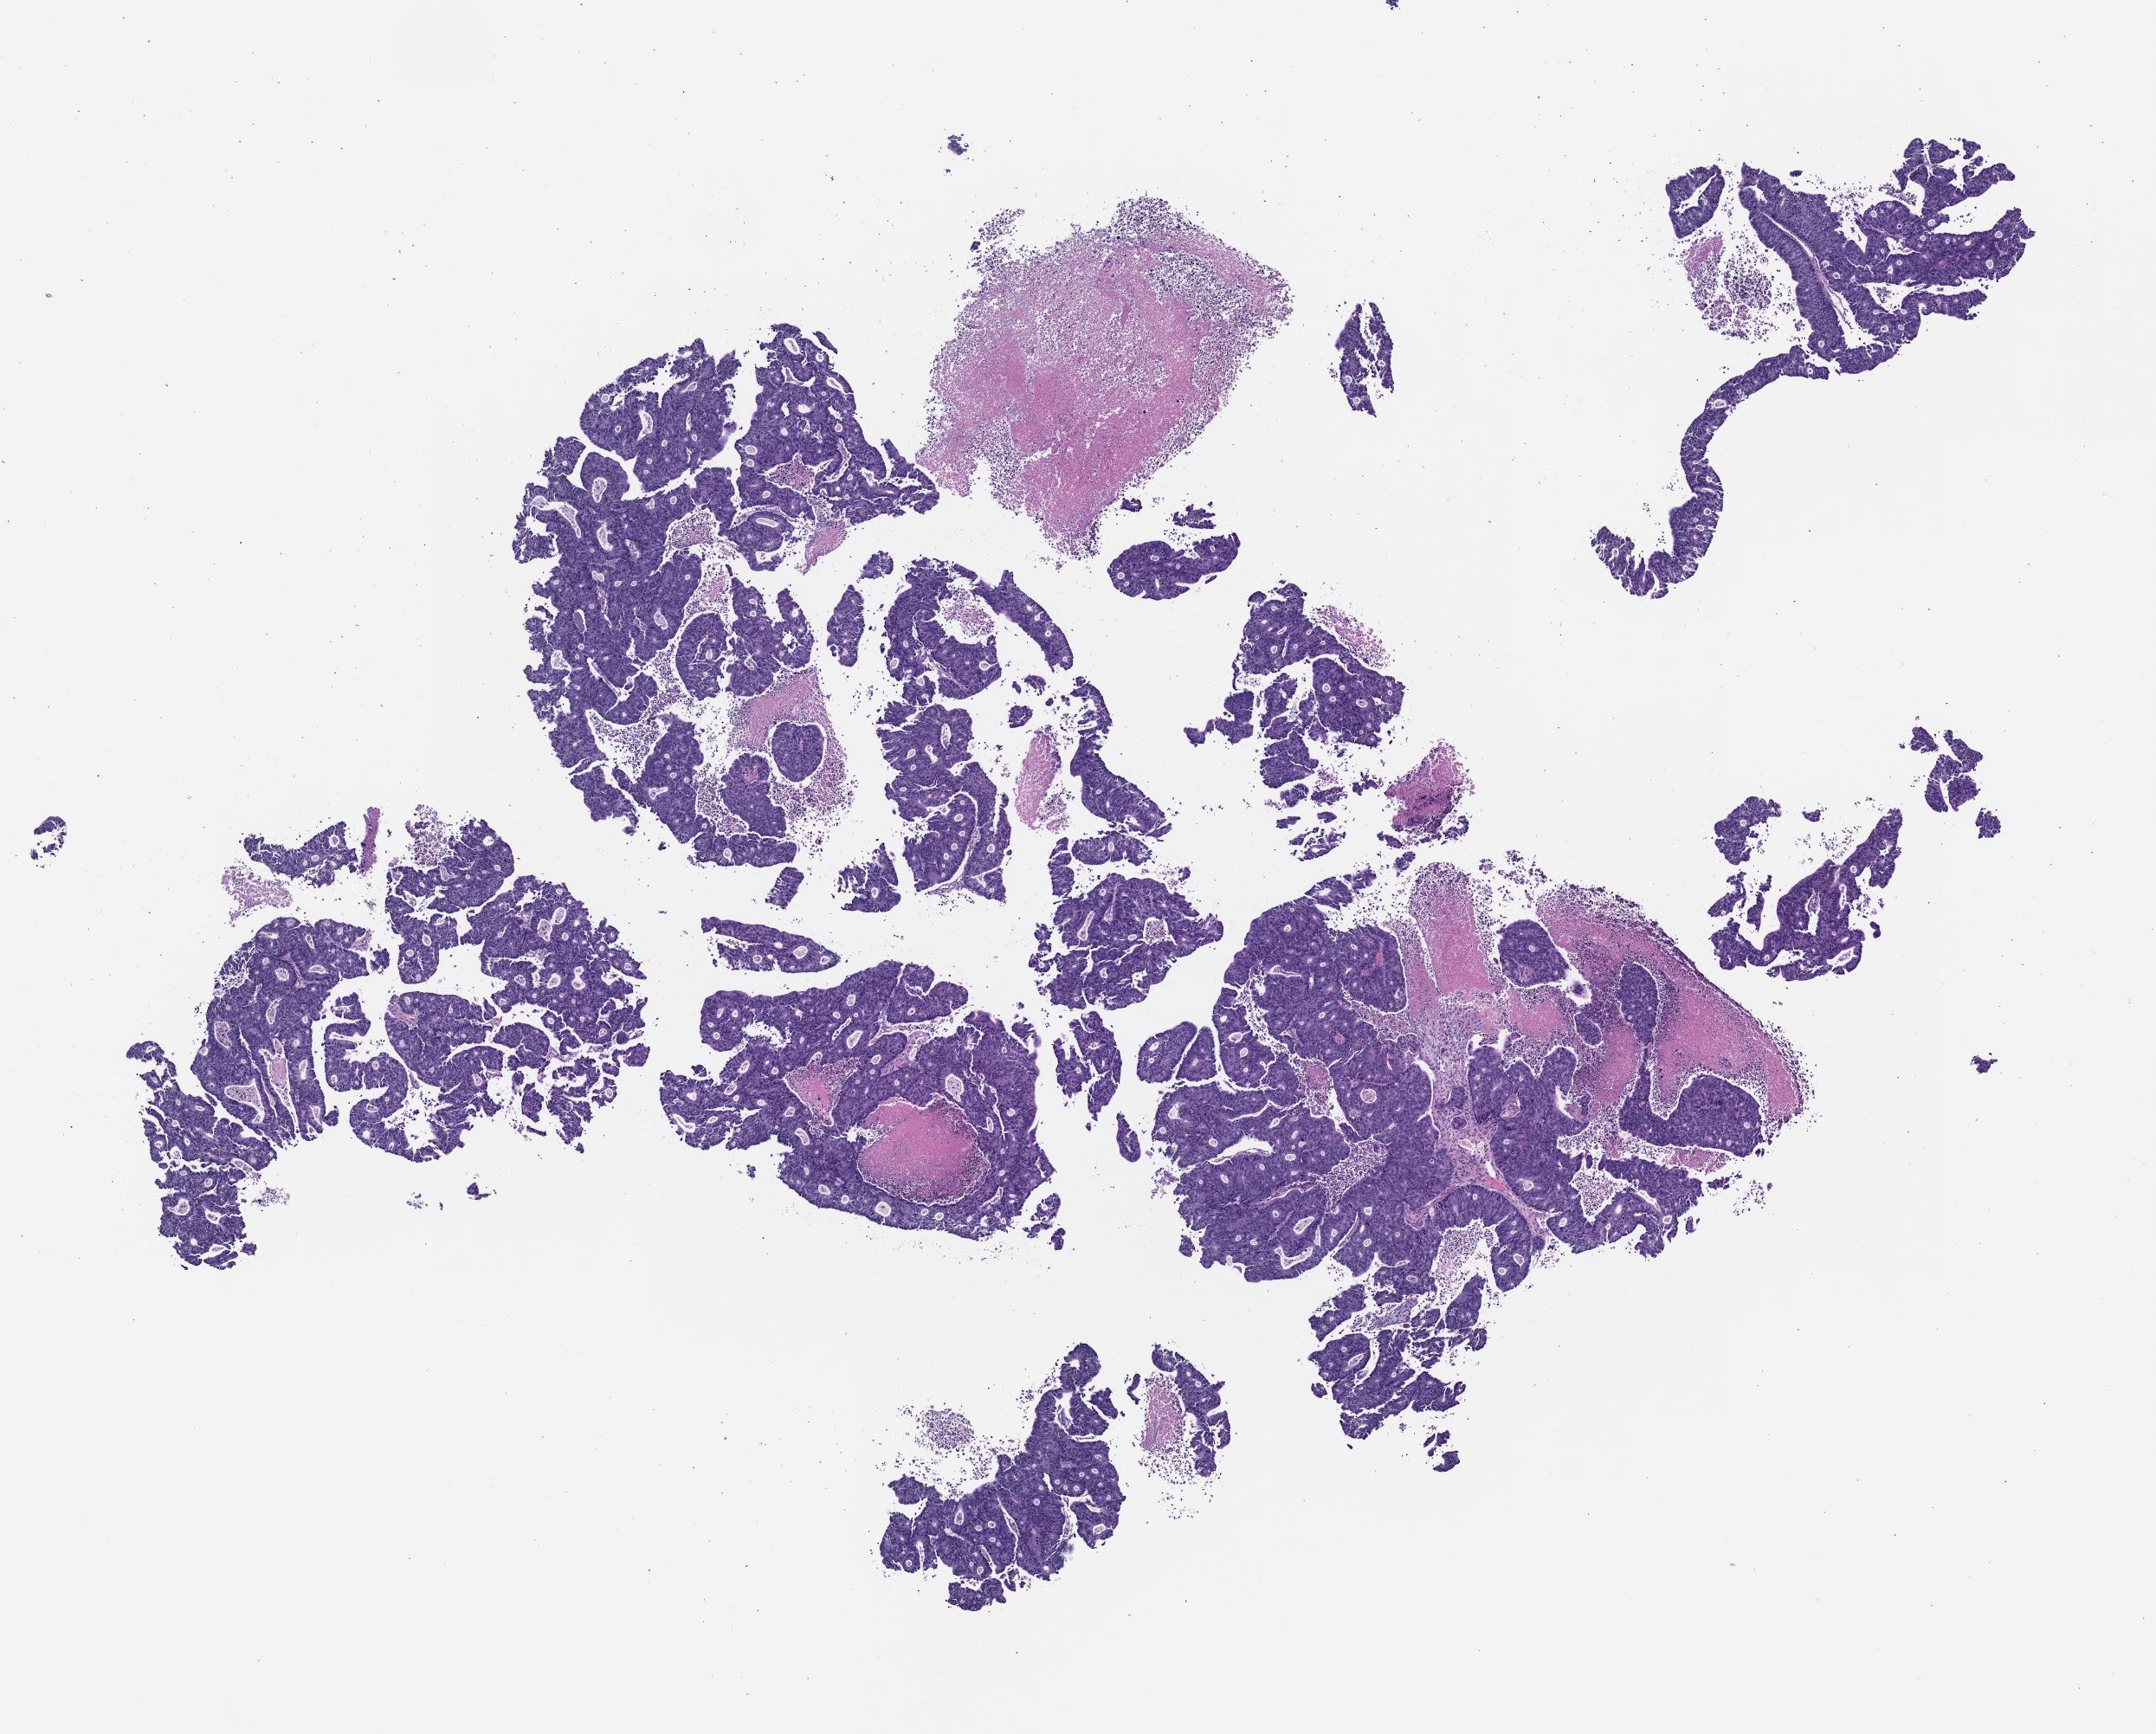
H&E whole-slide image of a patient-derived xenograft (PDX) tumor grown in a mouse, passage 3, a low-resolution overview of the entire scanned area, about 10.0 x 8.1 mm, formalin-fixed paraffin-embedded section, tumor site category: colon.
Originating patient diagnosis: Colon Adenocarcinoma.